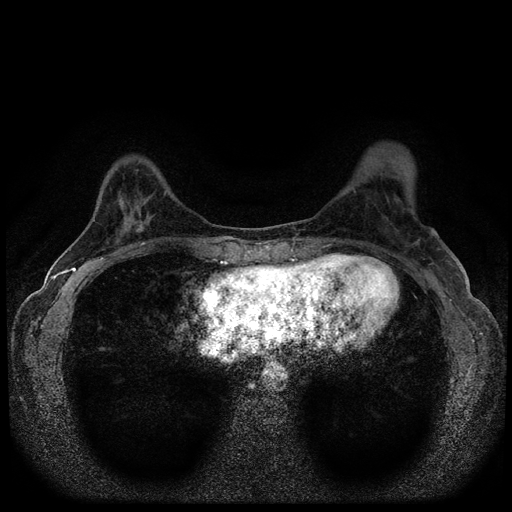
Breast MRI (dynamic contrast-enhanced, multi-phase), one axial slice. Position 33 of 116 along the scan axis. Dynamic contrast-enhanced series, time point 2 of 5 at this slice position (early post-contrast). 1.5 T. TE 2.7 ms, TR 5.6 ms. 512 × 512 image matrix, field of view 310 × 310 mm. Patient: female, 40 years.
Structures marked on this image (semi-automatically segmented with operator editing):
- breast lesion (labelled benign in the annotation): bounding box (x1, y1, x2, y2) in pixels: (127, 215, 150, 236)